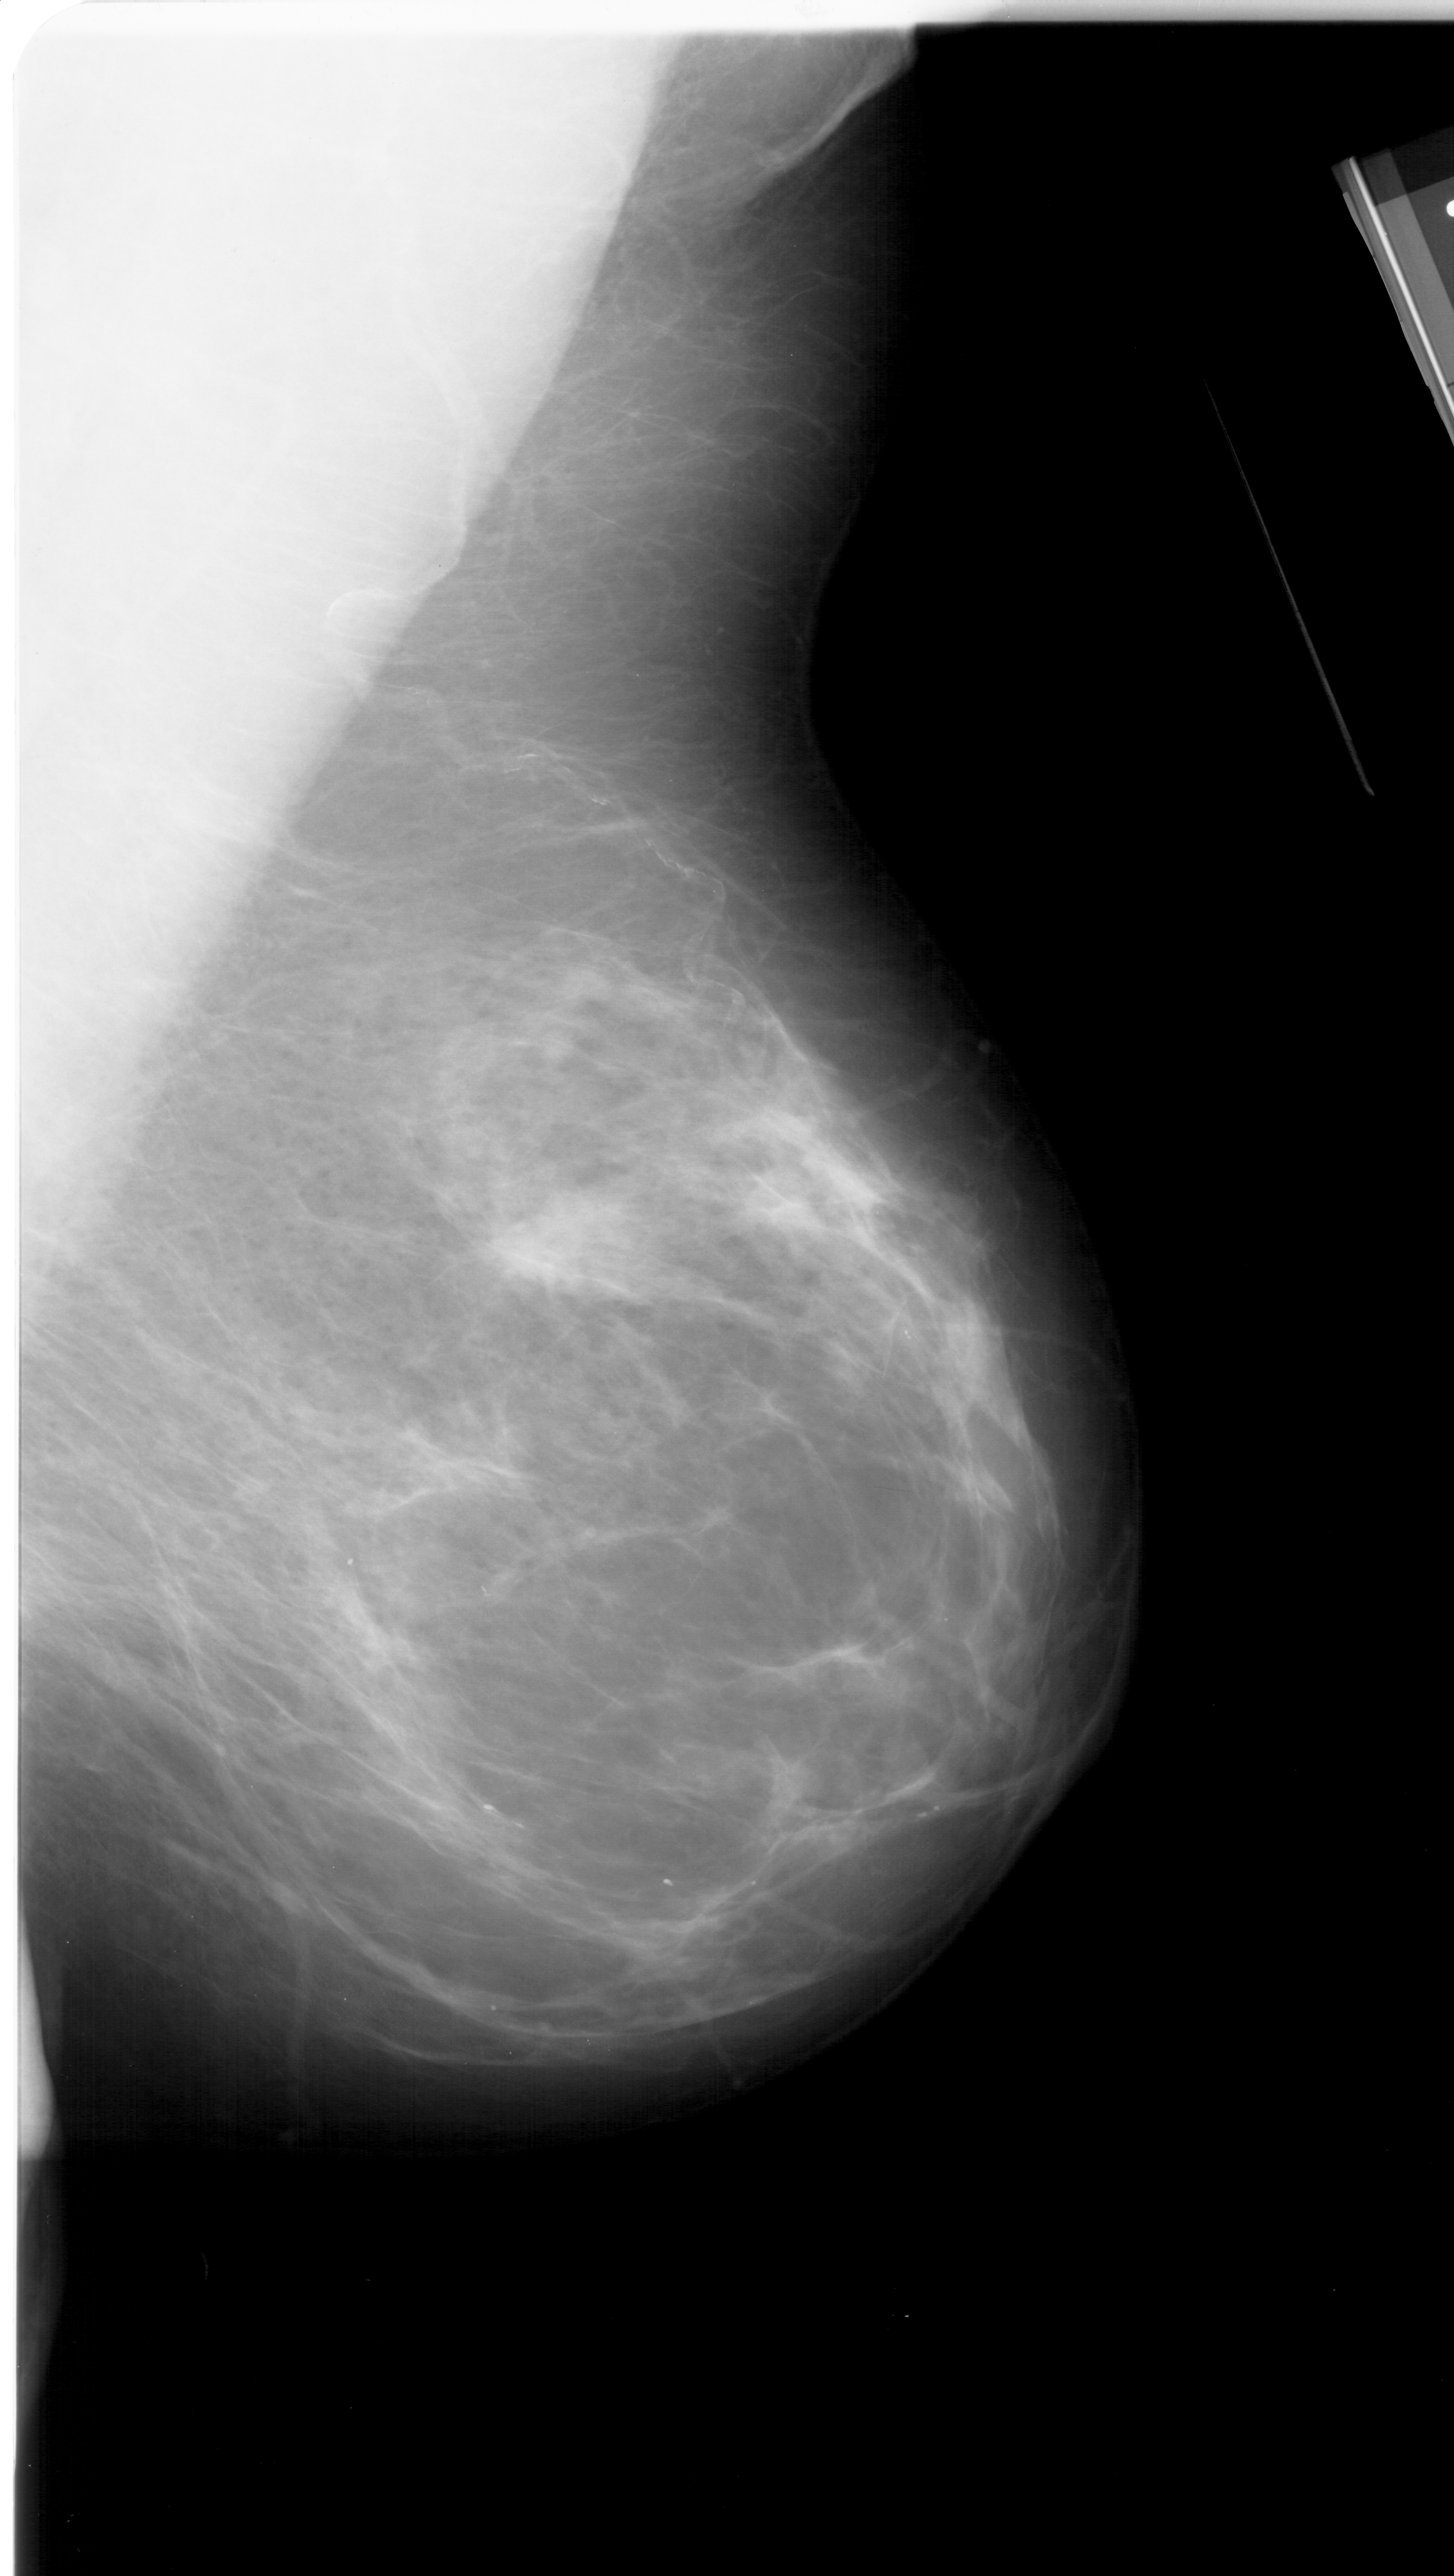
Mammogram (digitized film); right breast; MLO view; 1454 × 2576 image matrix.
Marked abnormalities (boxes around the expert regions of interest):
- mass, shape irregular, margins spiculated; BI-RADS assessment category 4; subtlety rating 4 on a 1 (subtle) to 5 (obvious) scale; pathology result (as recorded, not read from the image): malignant: box from (x=503, y=1194) to (x=610, y=1300) px